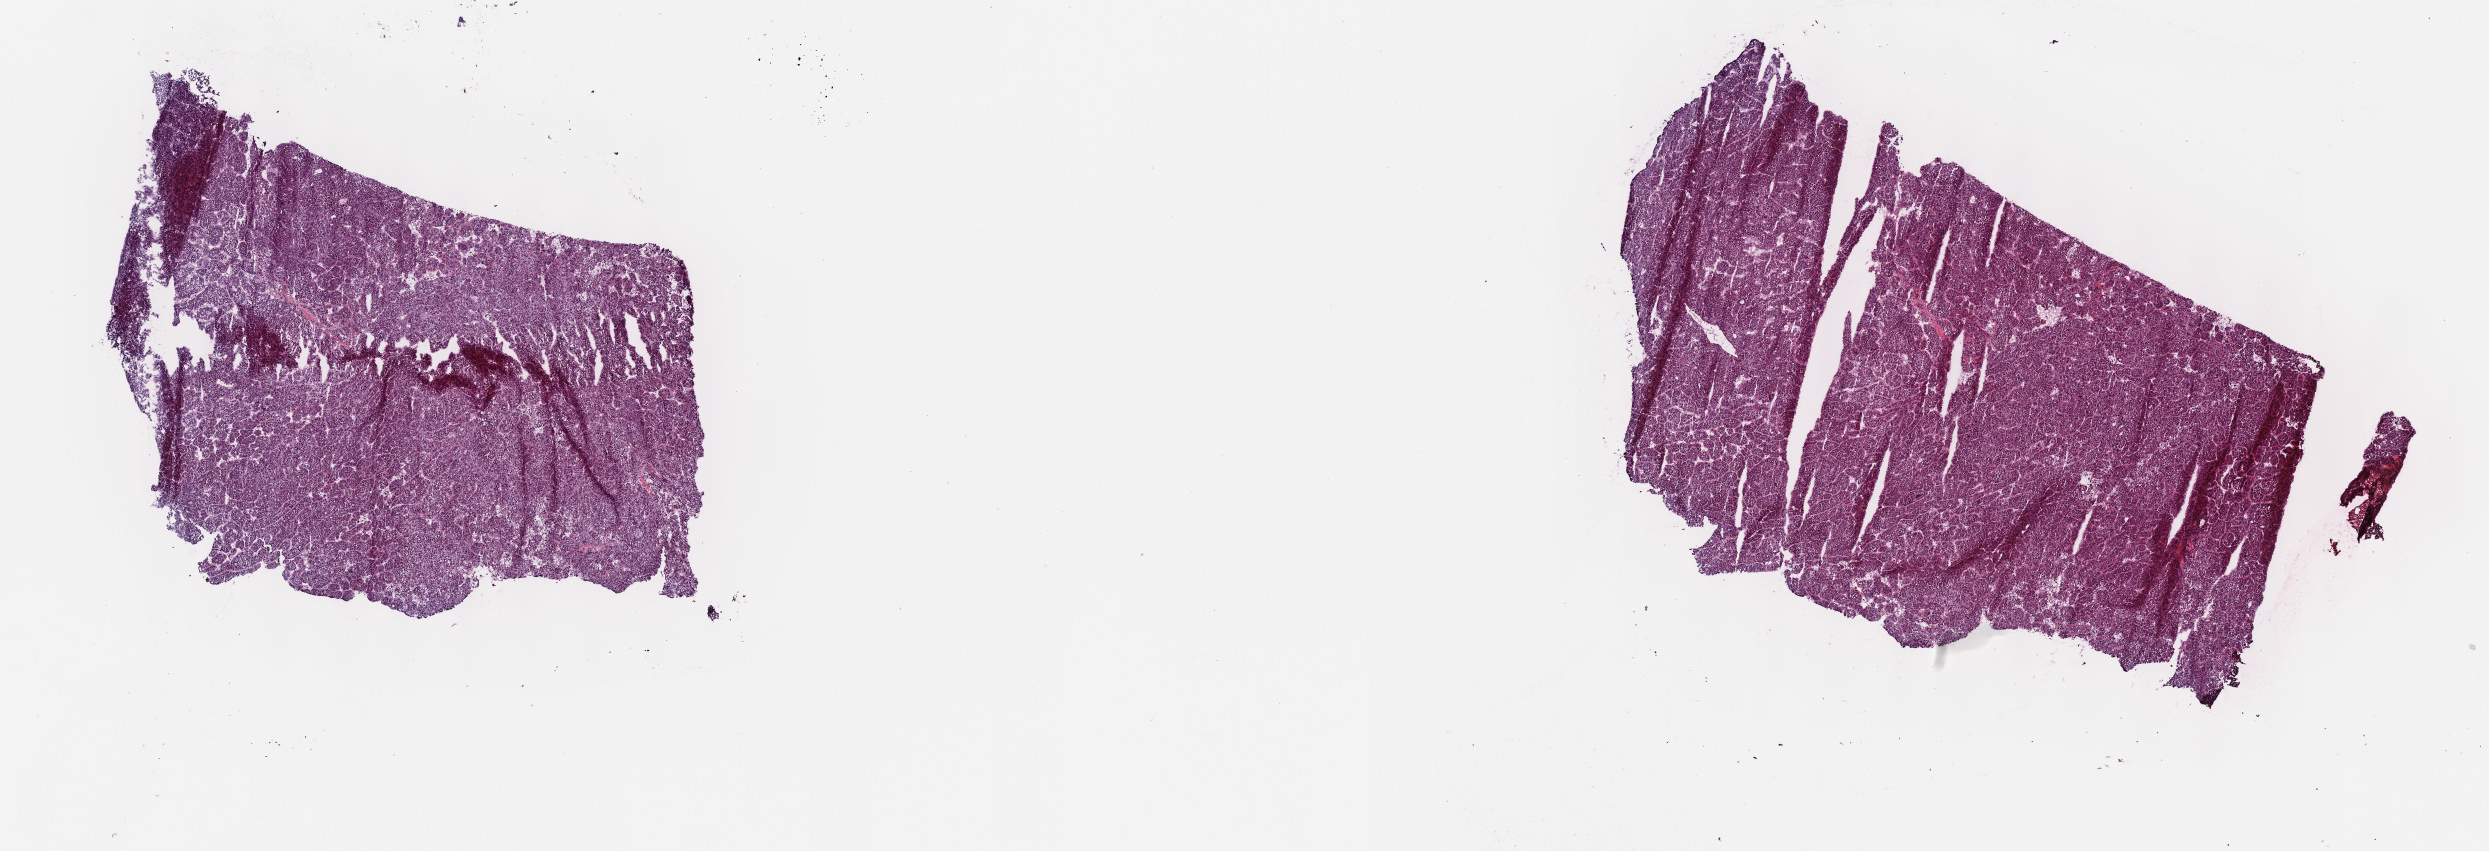
H&E-stained whole-slide image — whole scanned area (about 20.1 x 6.9 mm, slide scanned at 40x) shown as a low-resolution overview, frozen section from the top of the tissue portion, liver, primary tumour sample. Male, age 59 years at initial diagnosis. Histologic grade: G3 (poorly differentiated). Slide review estimates, as recorded: tumour cells 90%, tumour nuclei 95%, normal cells 0%, stromal cells 10%, necrosis 0%. Infiltration values recorded for this section: lymphocyte infiltration 0%, monocyte infiltration 0%, neutrophil infiltration 0%.
• AJCC pathologic stage: IIIA
• TNM: T3a N0 MX
• pathologic diagnosis: Hepatocellular carcinoma, NOS